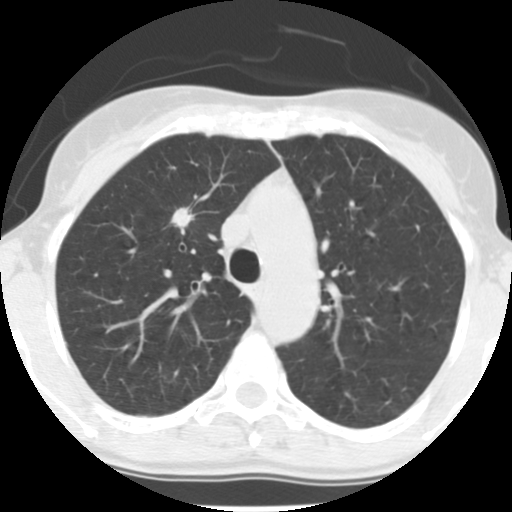
Chest CT (low-dose screening protocol), one axial image, second screening round (one year after baseline), lung window (W 1500 / L -600 HU), 2.5 mm slice thickness, slice 45 of 150 in the series, 512 × 512 image matrix, field of view 280 × 280 mm. Female, age 56 years at enrolment. Former smoker at enrolment.
- Expert reader's lesion annotation, bounding box (x1, y1, x2, y2) in pixels: (160, 198, 203, 243).
- Screening reader's record for this exam (one nodule recorded; not confirmed to be the boxed lesion): non-calcified nodule or mass ≥4 mm, right upper lobe, 12 × 9 mm, spiculated (stellate) margins, soft tissue attenuation, pre-existing on the prior screen: yes; interval growth: no.
- Lung cancer was diagnosed 350 days after this screen: adenocarcinoma, NOS, right upper lobe, moderately differentiated (G2), stage IA (AJCC 6th edition), 19 mm at pathology.